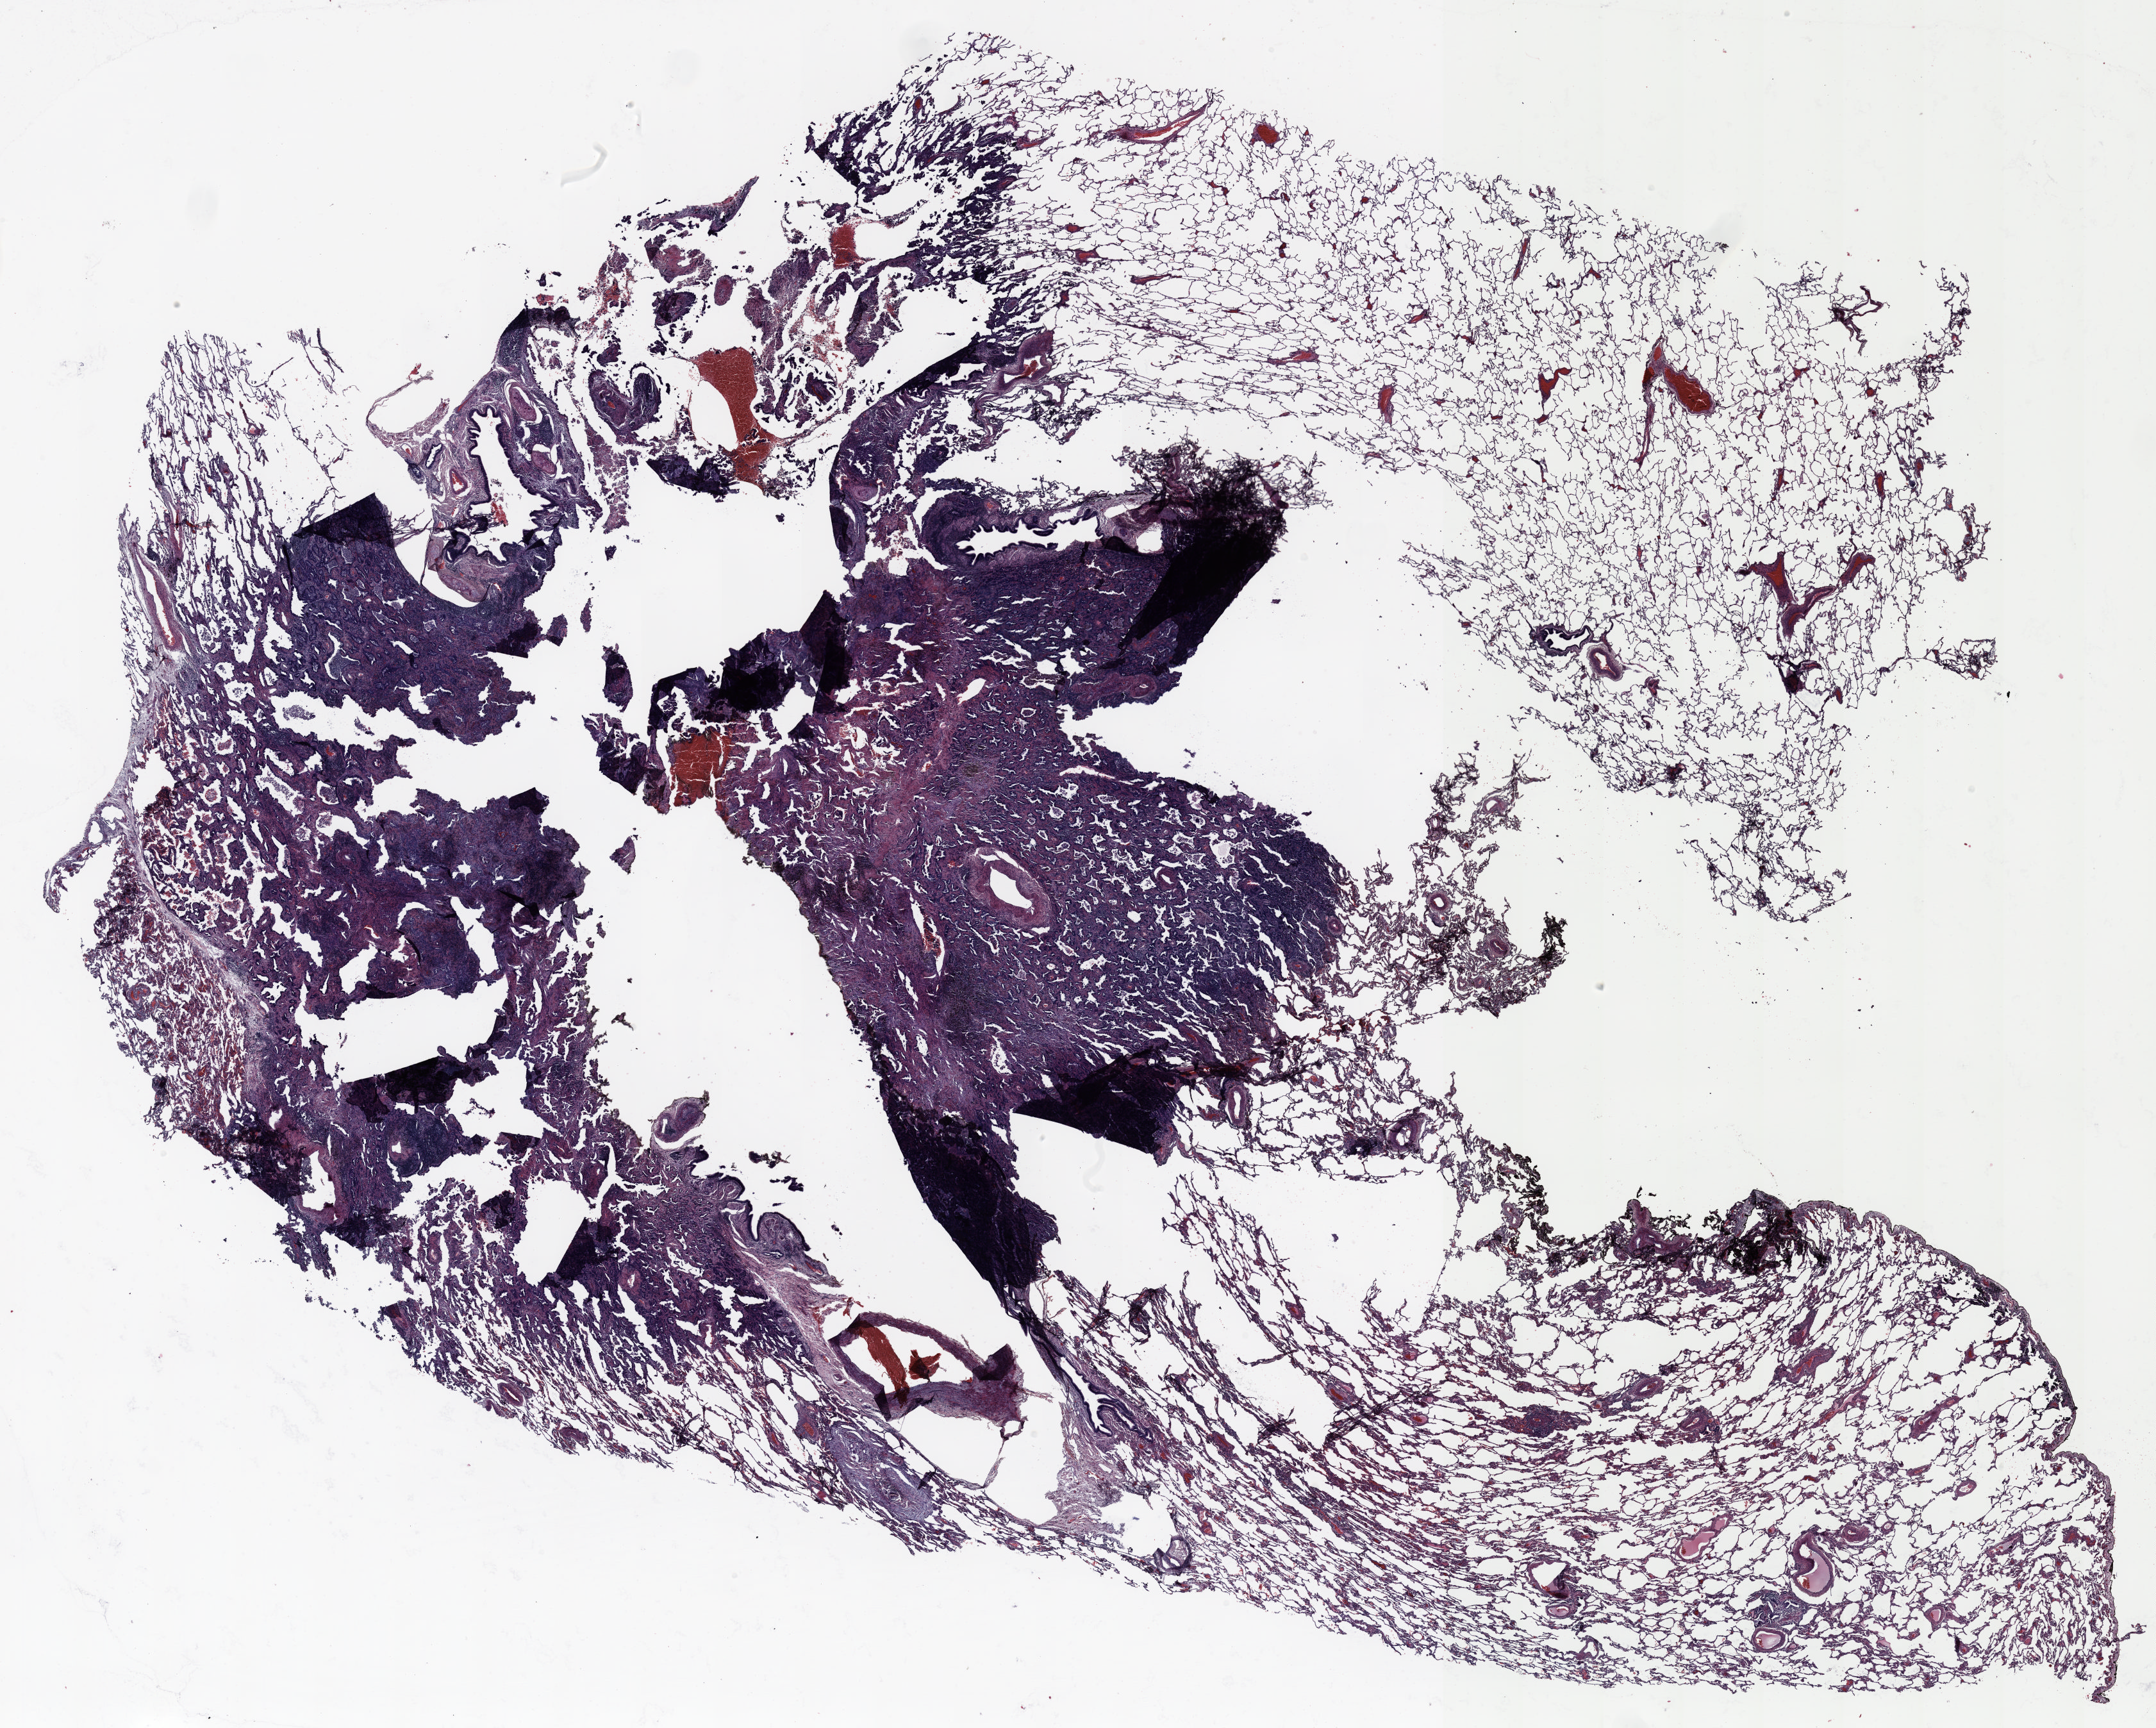
H&E whole-slide image — shown as a low-resolution overview of the whole scanned area (about 27.0 x 21.7 mm, from a 20x scan). Formalin-fixed paraffin-embedded (FFPE) section. Lung tissue. Male, age 62 at enrolment. Current smoker at enrolment. Grade: moderately differentiated (G2).
Stage (AJCC 6th edition): IA. Participant's lung-cancer diagnosis: Adenocarcinoma, NOS. Primary tumour location (clinical record): left lower lobe. Tumour size (pathology): 30 mm.